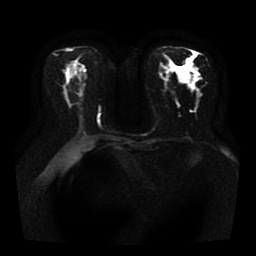
Breast MRI, one axial slice; slice 19 of 41 in the series (ordered by position); diffusion-weighted series; image 2 of 4 stored at this slice position (different b-values; order by instance number); 1.5 T; 256 × 256 image matrix, field of view 330 × 330 mm. Female patient.
Outlined on this slice (outlined manually by an expert reader):
- tumour on diffusion-weighted imaging: bounding box [x1, y1, x2, y2] px = [184, 68, 201, 82]